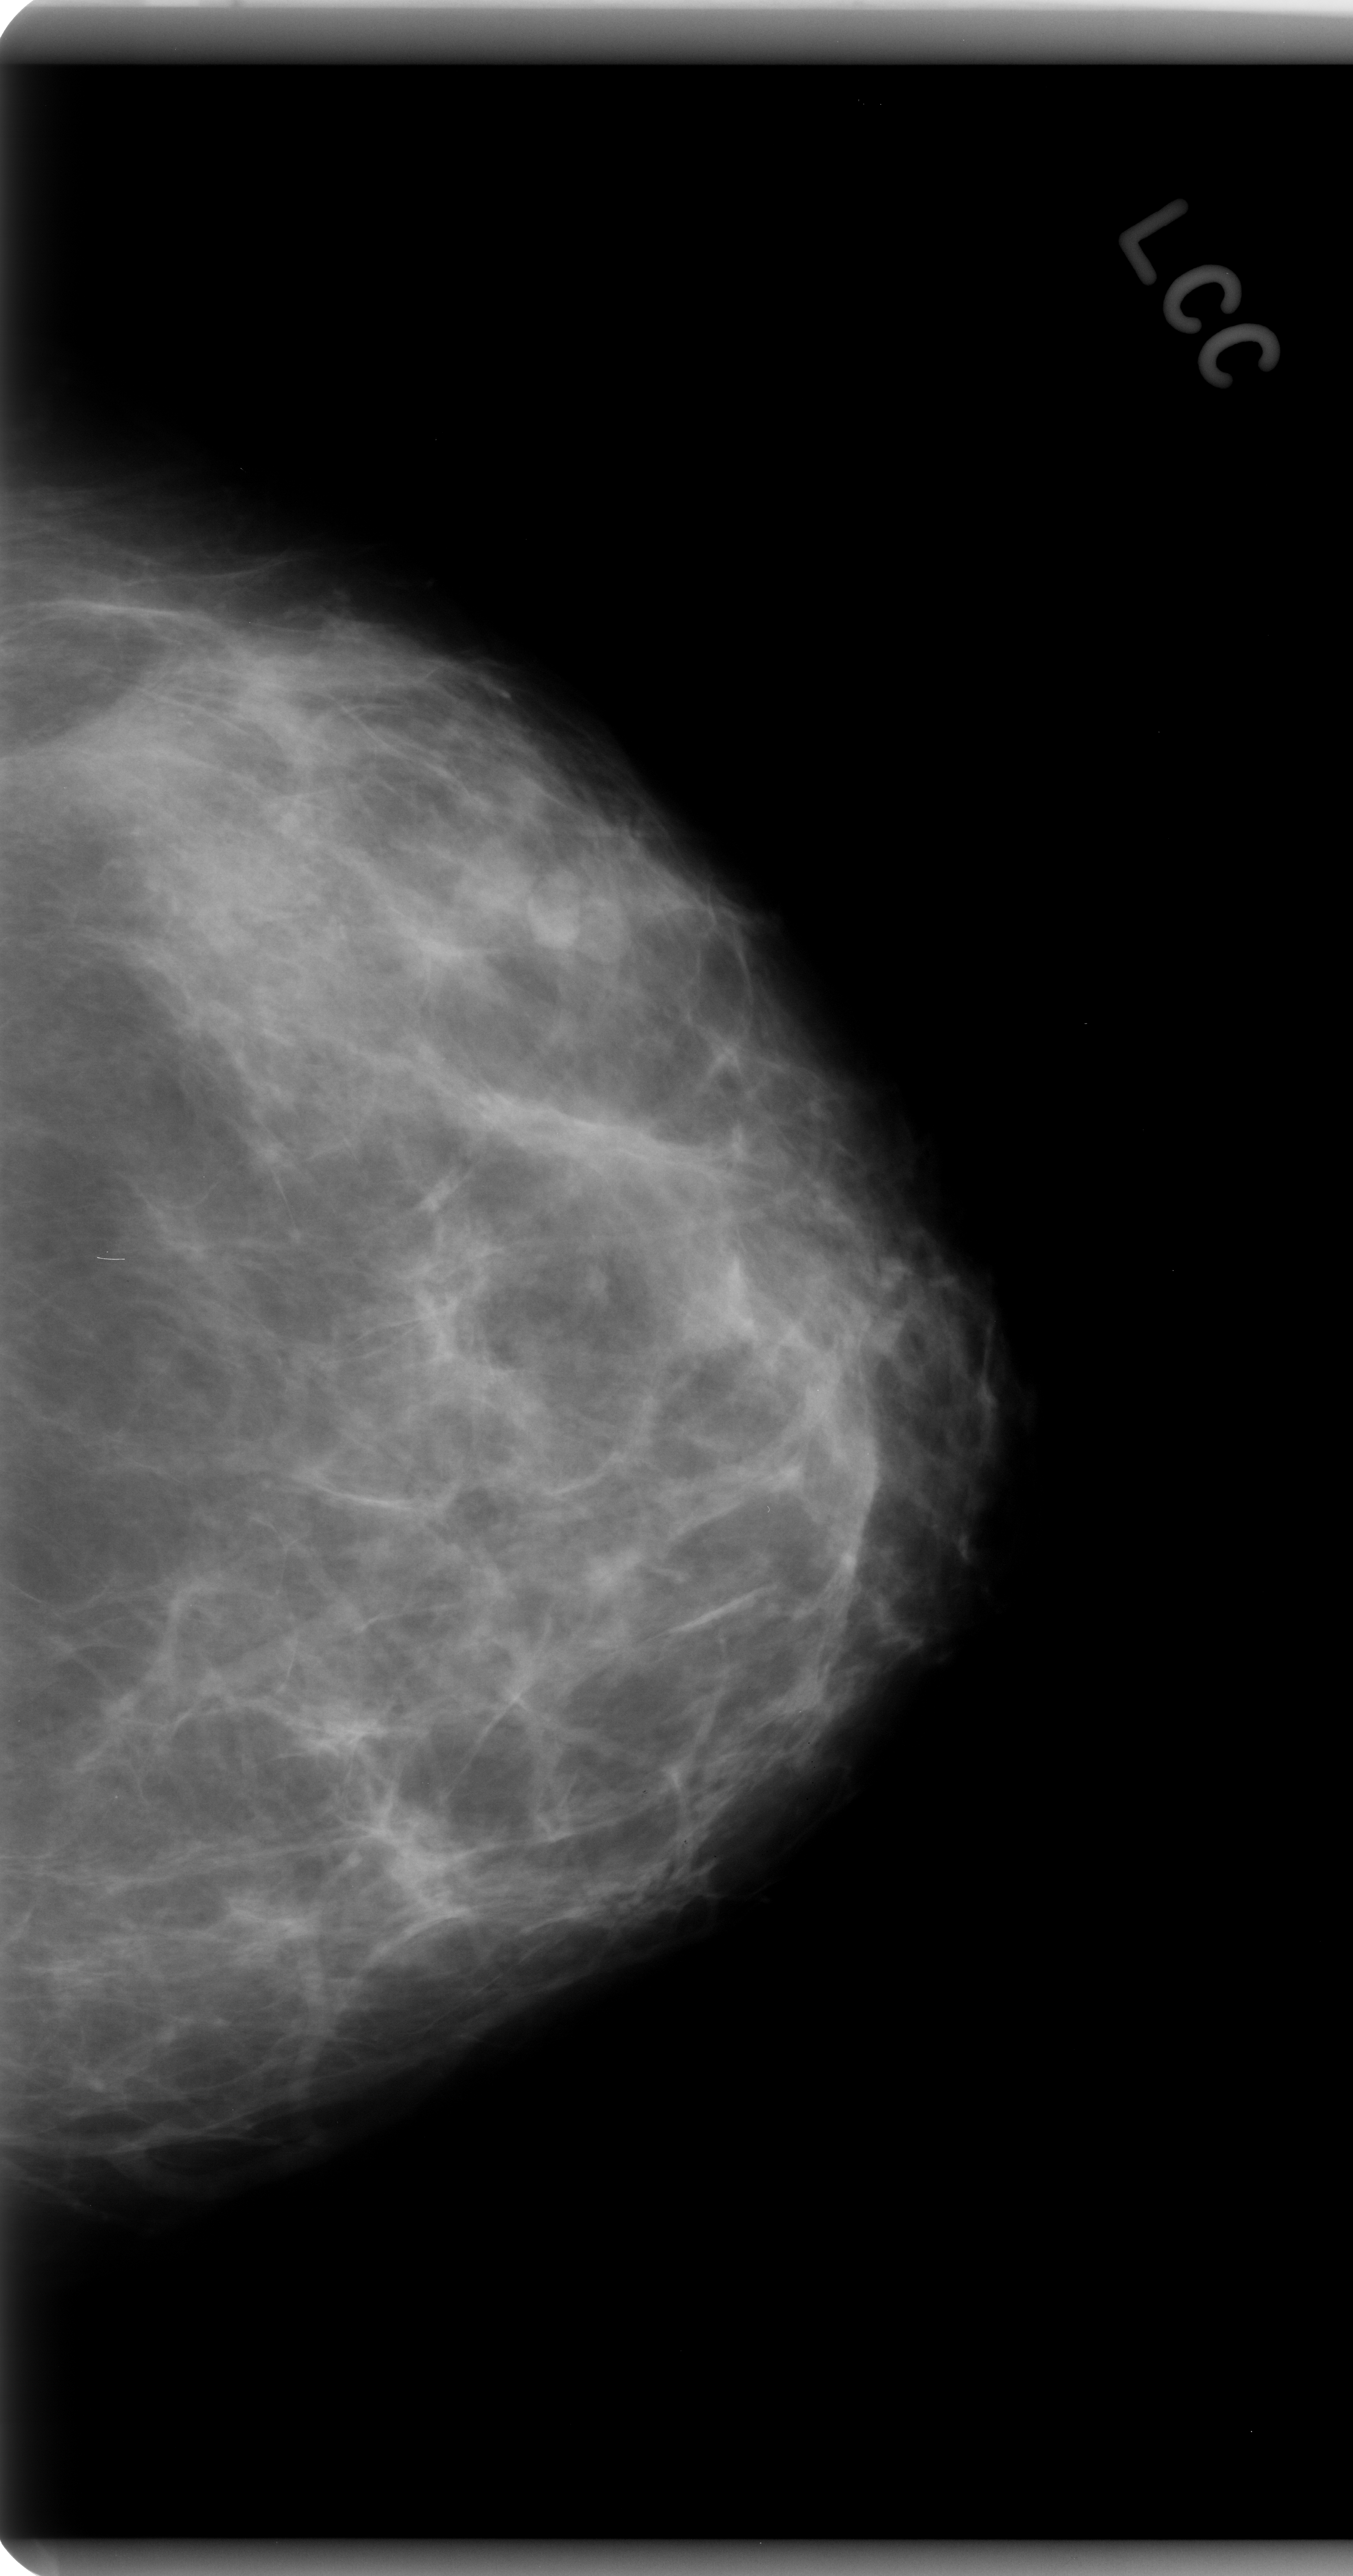
Digitized screen-film mammogram, left breast, craniocaudal (CC) view, BI-RADS breast density category 2 (scale 1–4).
Radiologist-marked abnormalities on this image: mass, shape lobulated, margins circumscribed; BI-RADS assessment category 3; pathology (as recorded): benign.